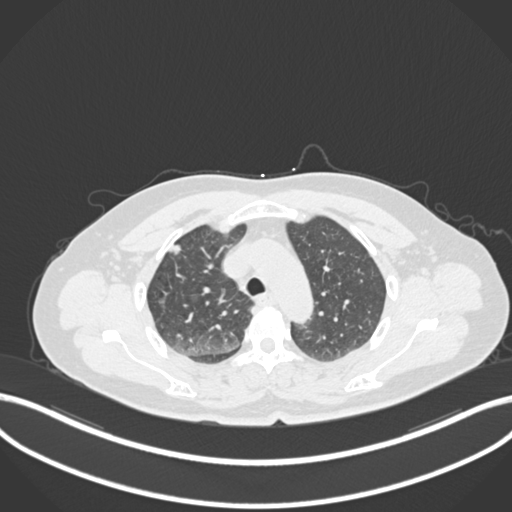
Chest CT, one axial slice. Slice 174 of 223 in the series (ordered by position). Reconstruction kernel B30f. 120 kVp. Lung window (W 1500 / L -600 HU). 1 mm slice thickness. 512 × 512 image matrix, field of view 400 × 400 mm. Patient: female, 56 years. From the clinical record (not read from this slice): clinical TNM (as recorded): T1c N0 M0.
Annotated regions visible in this slice (rectangle marked by the reading radiologist):
- lung tumour (recorded histology: adenocarcinoma): bounding box (x1, y1, x2, y2) in pixels: (165, 238, 188, 254)